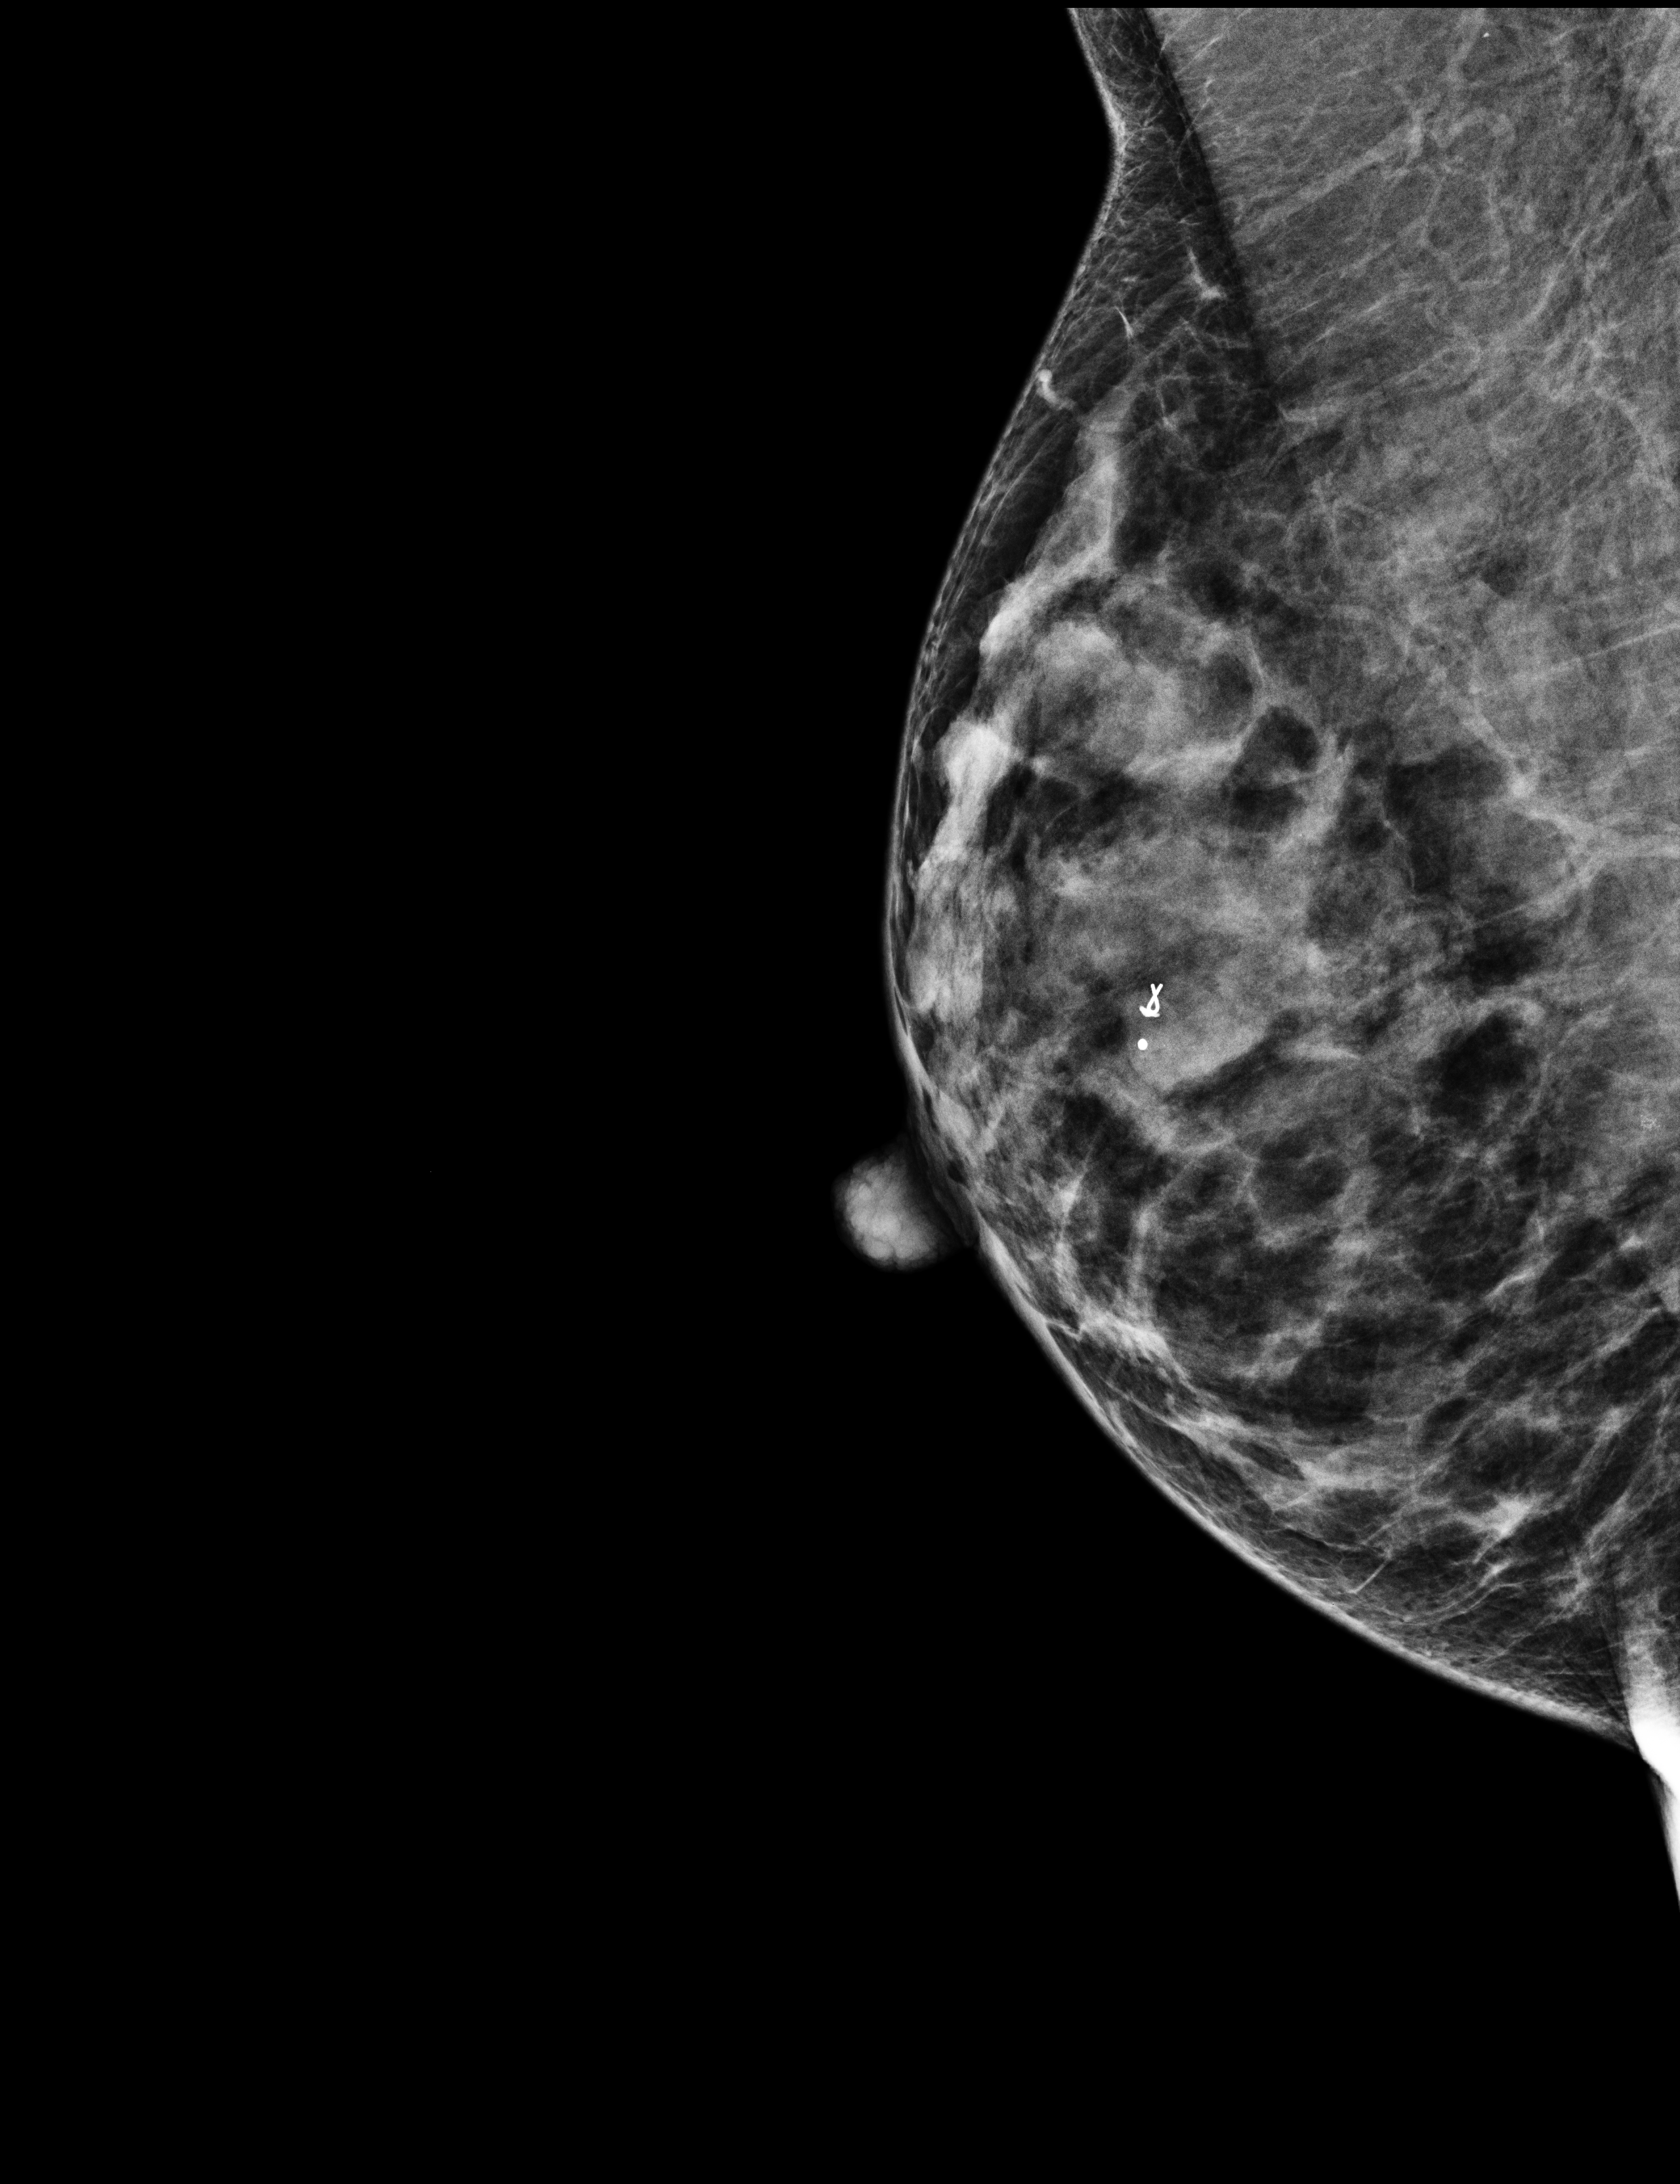
Annual screening mammography examination. Patient: female, 54 years.
Image type: full-field digital mammogram. Breast: right. Projection: mediolateral oblique (MLO) view.